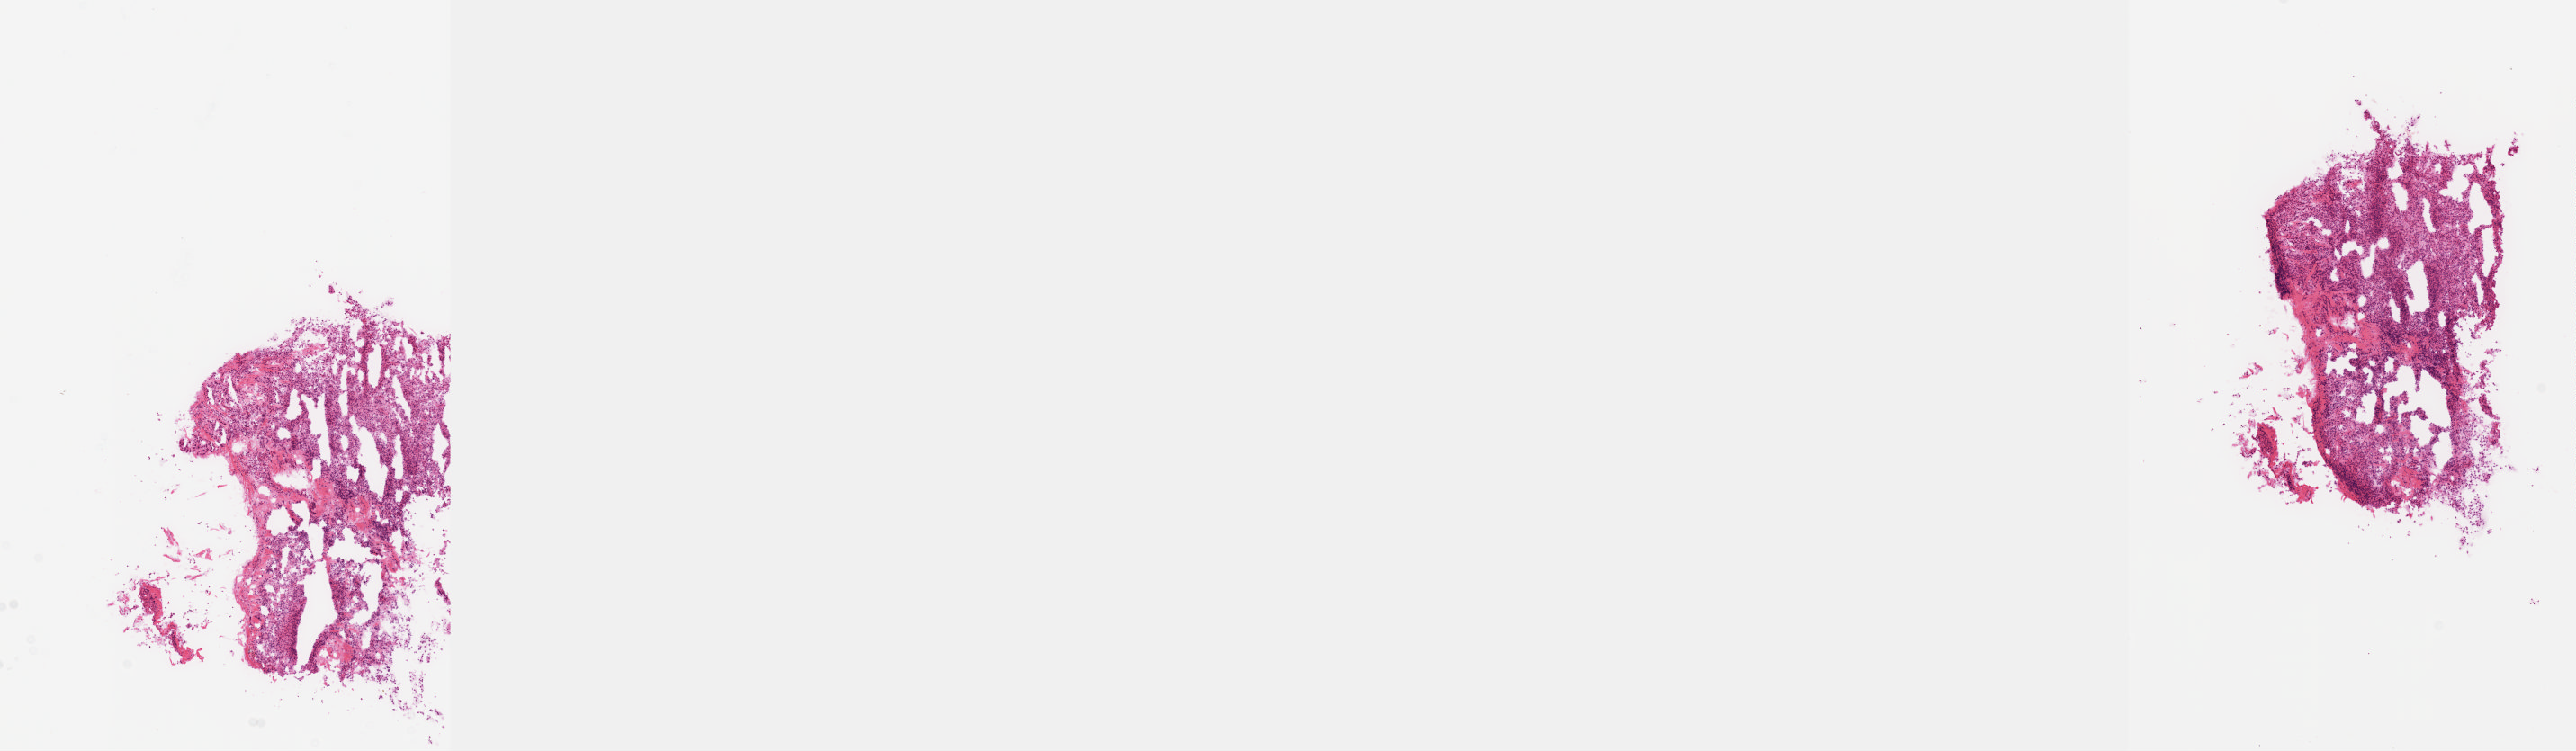
Whole-slide histology image, H&E-stained, low-resolution overview of the scanned area, about 23.1 x 6.7 mm (acquisition: 20x scan), frozen section from the top of the tissue portion, adrenal gland, primary tumour sample. Female patient; age at initial diagnosis 52 years. Composition of this section per pathologist review: tumour cells 80%, tumour nuclei 80%, normal cells 0%, stromal cells 20%, necrosis 0%. Infiltration values recorded for this section: lymphocyte infiltration 2%, monocyte infiltration 1%, neutrophil infiltration 1%.
Diagnosis: Pheochromocytoma, NOS.